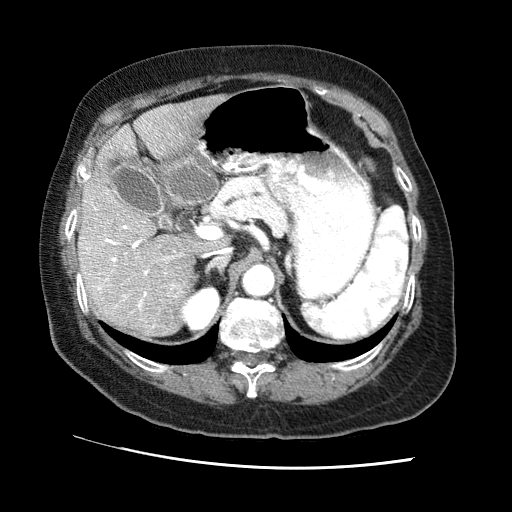
Contrast-enhanced abdominal CT (liver protocol), one axial slice. Position 37 of 65 along the scan axis. Soft-tissue window (W 400 / L 40 HU). 512 × 512 image matrix. Case-level facts recorded for this patient, not image findings: diagnosis: hepatocellular carcinoma (patient treated with transarterial chemoembolisation; whether this scan precedes or follows treatment is not stated here); TNM stage (as recorded): Stage-II; Child-Pugh class: A.
Annotated regions visible in this slice (semi-automatically segmented with operator editing):
- liver parenchyma outside the tumour (the mass and vessels are separate outlines, so this box may not span the whole liver): bounding box [x1, y1, x2, y2] px = [78, 94, 226, 338]
- liver vessels: [85, 146, 178, 310]